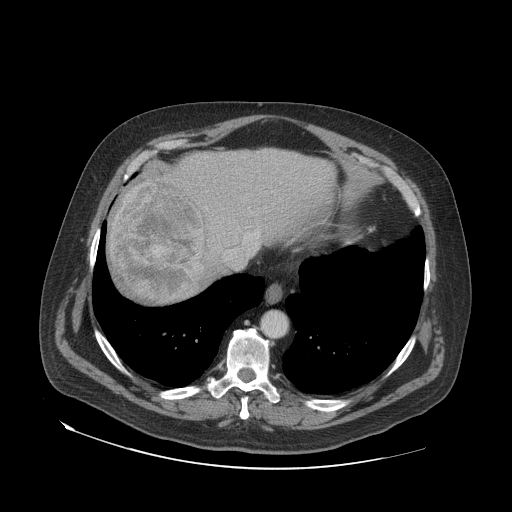
Contrast-enhanced abdominal CT (liver protocol), one axial slice. Slice 64 of 79 in the series (ordered by position). Reconstruction kernel STANDARD. 140 kVp. Soft-tissue window (W 400 / L 40 HU). 512 × 512 image matrix, field of view 480 × 480 mm. Case-level facts recorded for this patient, not image findings: diagnosis: hepatocellular carcinoma (patient treated with transarterial chemoembolisation; whether this scan precedes or follows treatment is not stated here); TNM stage (as recorded): Stage-IVA; Child-Pugh class: A; tumour nodularity: multinodular.
Outlined on this slice (semi-automatic segmentation, software-assisted and operator-edited):
- abdominal aorta: bounding box [x1, y1, x2, y2] px = [261, 312, 287, 337]
- liver parenchyma outside the tumour (the mass and vessels are separate outlines, so this box may not span the whole liver): [106, 148, 336, 302]
- mass: [111, 180, 206, 299]
- liver vessels: [256, 235, 259, 238]